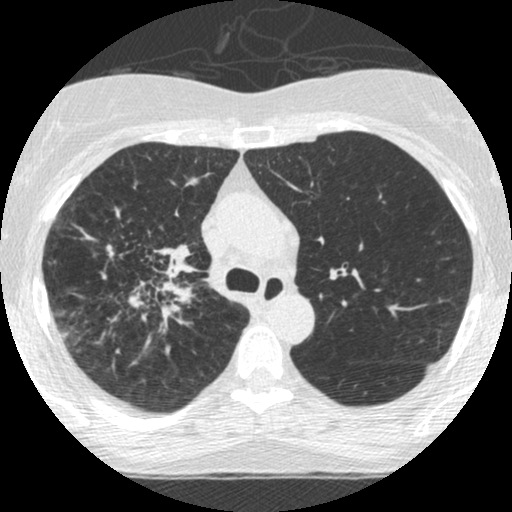
Low-dose screening chest CT, one axial slice; position 181 of 253 along the scan axis; lung window (W 1500 / L -600 HU); 512 × 512 image matrix, field of view 294 × 294 mm.
Structures marked on this image (expert manual segmentation):
- lesion 2 (tumor, hilum of right lung): bounding box [x1, y1, x2, y2] px = [129, 244, 197, 333]